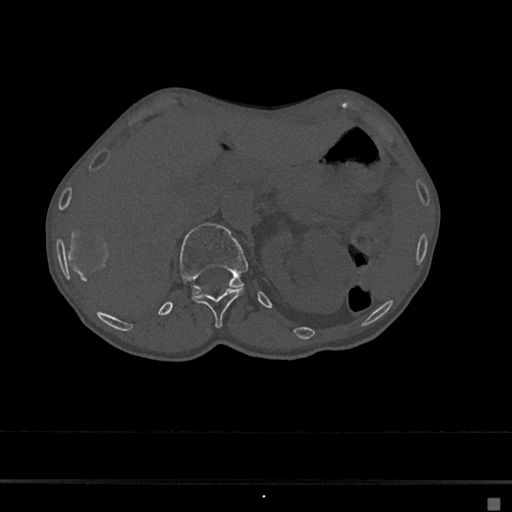
CT including the spine, one axial slice. Position 97 of 797 along the scan axis. Reconstruction kernel Br40s/3. 120 kVp. Bone window (W 1800 / L 400 HU). 512 × 512 image matrix. Patient: female, 68 years. From the clinical record (not read from this slice): primary cancer: renal.
Outlined on this slice (semi-automatically segmented with operator editing):
- L1 vertebra: box from (x=179, y=223) to (x=249, y=295) px
- T12 vertebra: (x=193, y=288)–(x=244, y=329)